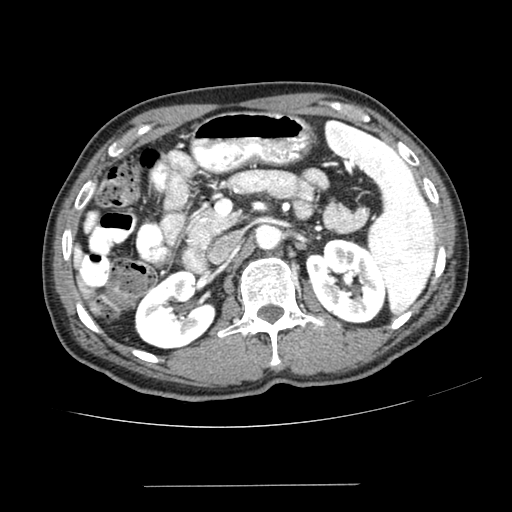
Contrast-enhanced abdominal CT (liver protocol), one axial slice. Position 134 of 187 along the scan axis. 100 kVp. One of 2 acquisitions stored at this slice position. Soft-tissue window (W 400 / L 40 HU). 2.5 mm slice thickness. 512 × 512 image matrix, field of view 360 × 360 mm. Case-level facts recorded for this patient, not image findings: diagnosis: hepatocellular carcinoma (patient treated with transarterial chemoembolisation; whether this scan precedes or follows treatment is not stated here); TNM stage (as recorded): Stage-I; Child-Pugh class: A; tumour differentiation: poorly differentiated; tumour nodularity: uninodular.
Annotated regions visible in this slice (semi-automatically segmented with operator editing):
- liver parenchyma outside the tumour (the mass and vessels are separate outlines, so this box may not span the whole liver): bounding box <72,245,90,298> (left, top, right, bottom; pixels)
- liver vessels: <76,250,80,257>